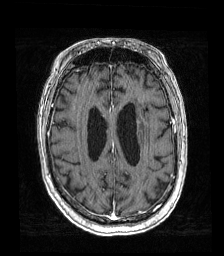
Brain MRI from a brain-tumour surgery series, one axial slice; position 60 of 192 along the scan axis; T1-weighted post-contrast; 1 mm slice thickness; 224 × 256 image matrix, field of view 219 × 250 mm. From the clinical record (not read from this slice): histopathology: Metastatic carcinoma from lung primary; tumour location: Left Frontal Caudate.
Annotated regions visible in this slice (expert manual segmentation):
- tumour: bounding box (x1, y1, x2, y2) in pixels: (137, 122, 140, 129)